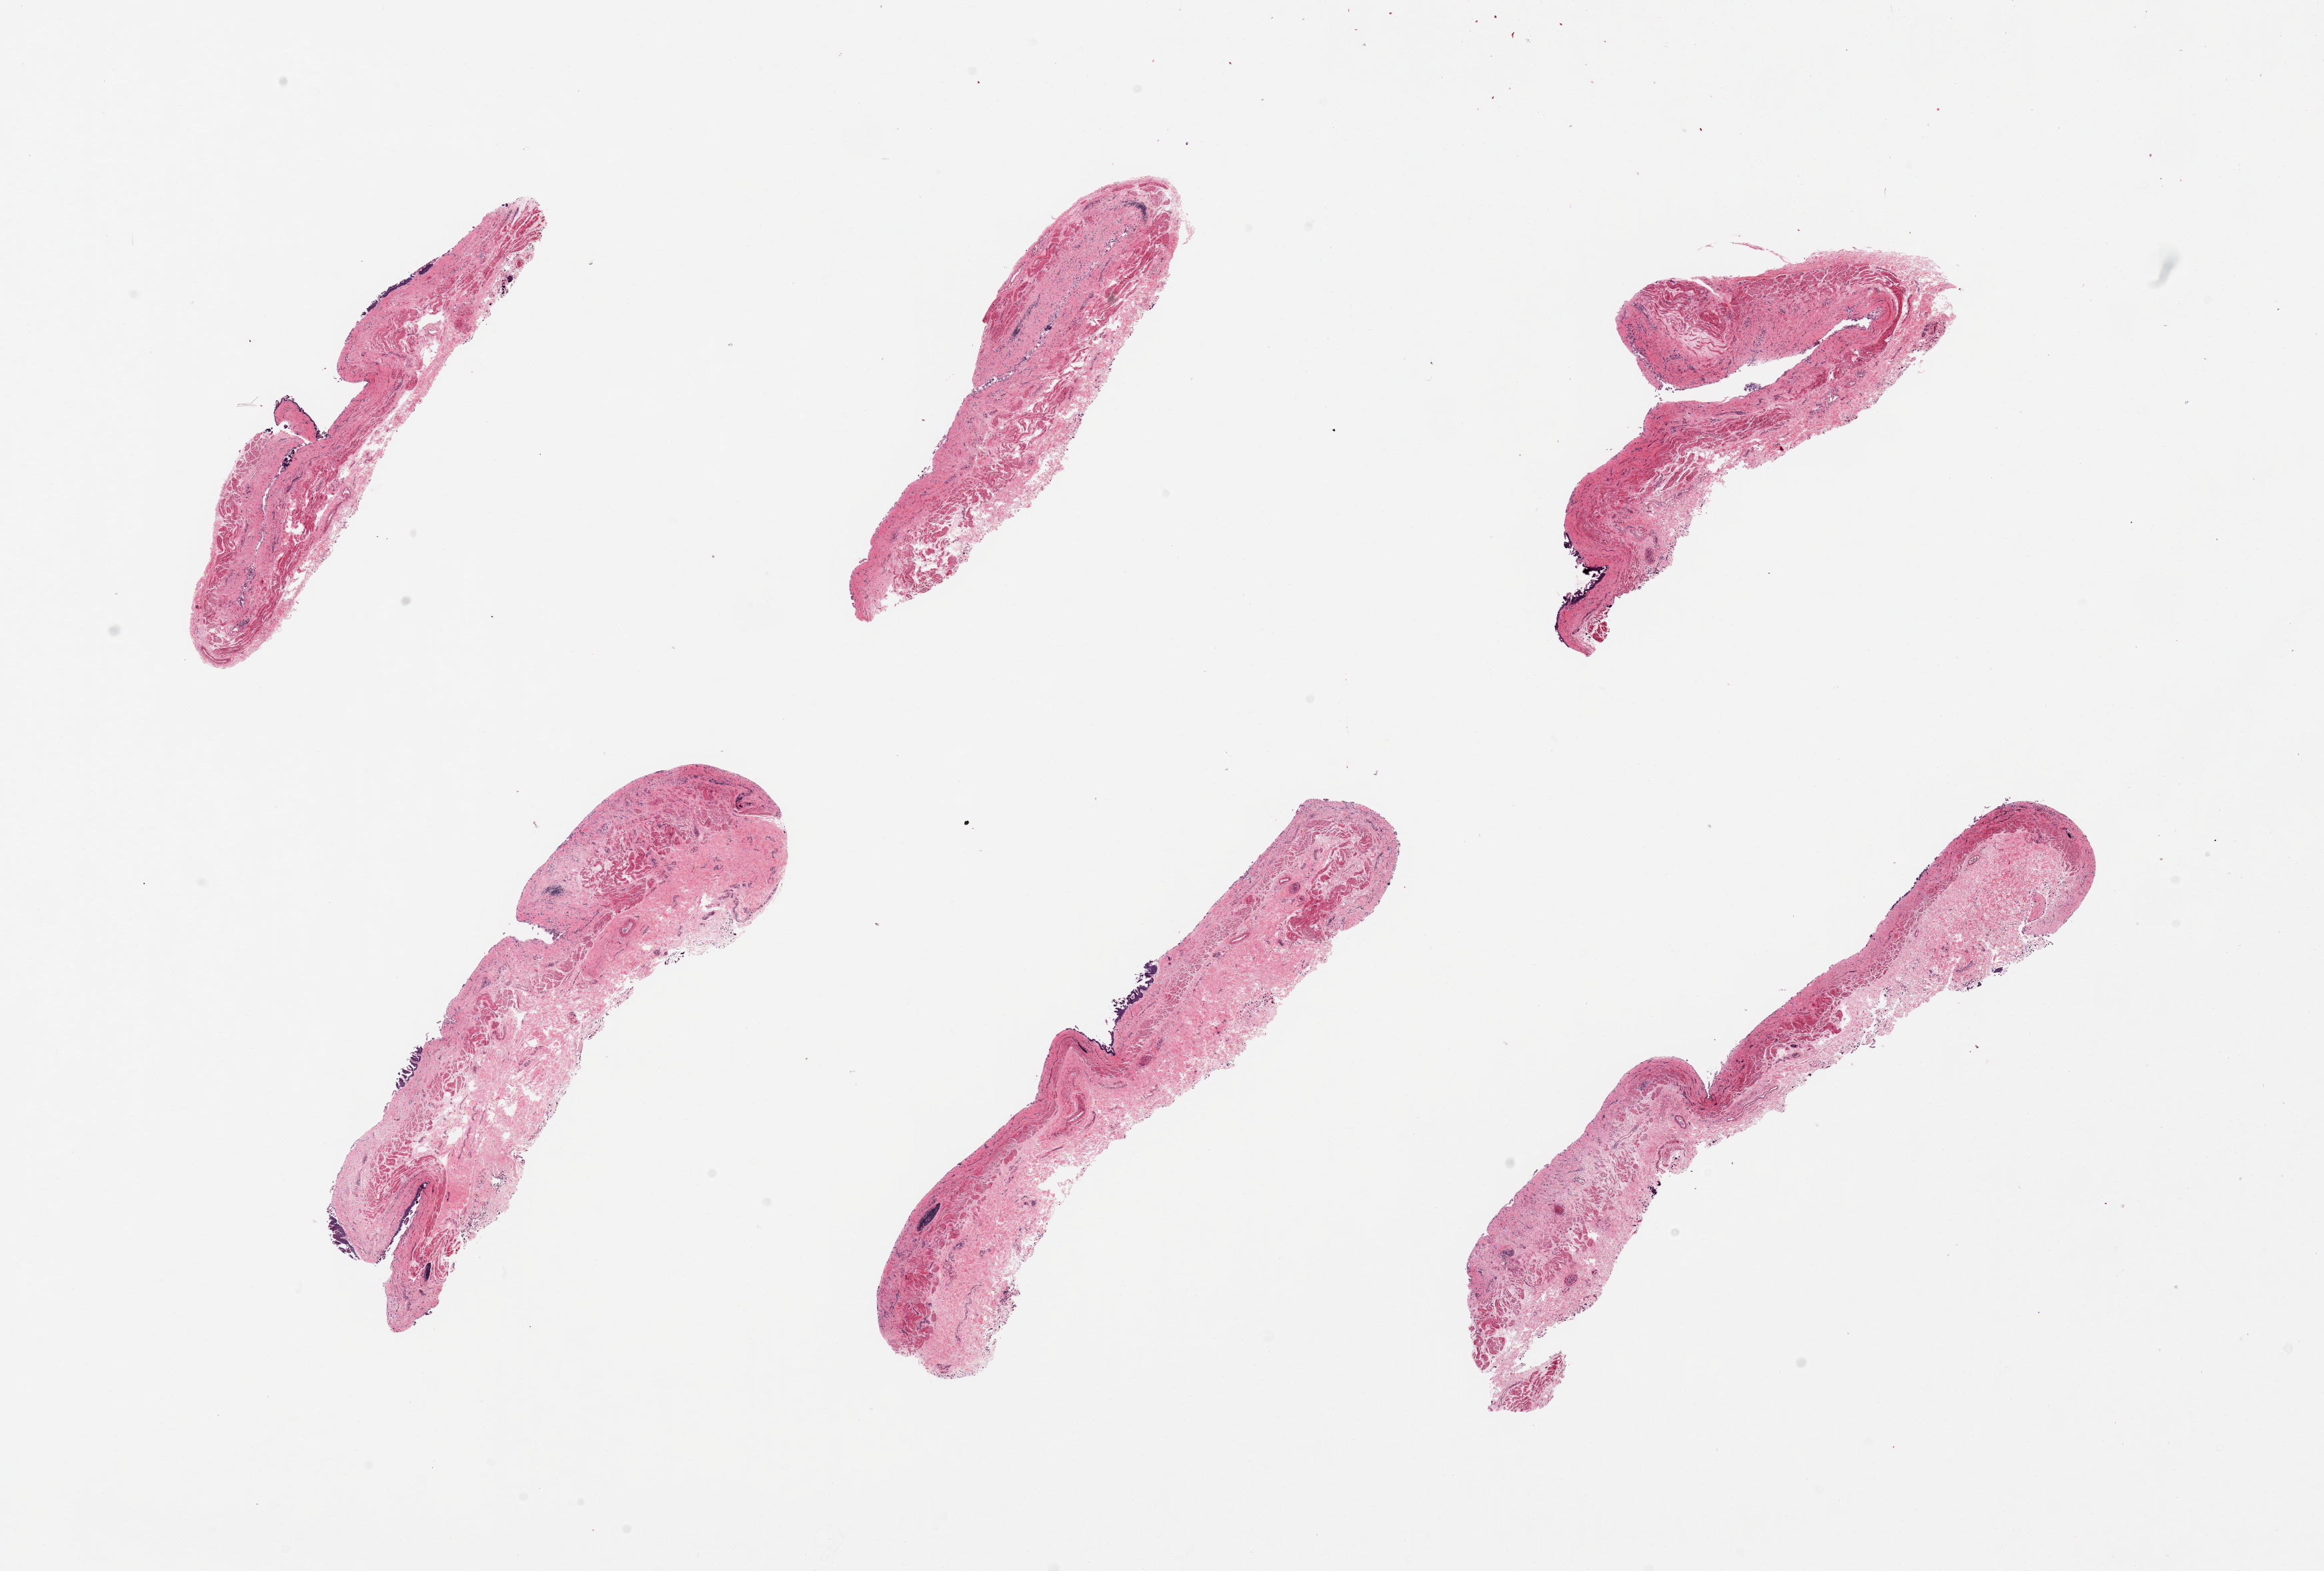
Digitized hematoxylin and eosin (H&E)-stained section, shown as a low-resolution overview of the whole scanned area (about 27.6 x 18.6 mm, from a 20x scan); PAXgene-fixed paraffin-embedded (PFPE) section; section of esophageal muscle (target tissue); donor tissue sample.
Pathologist's review note for this sample: 6 pieces, all muscularis.